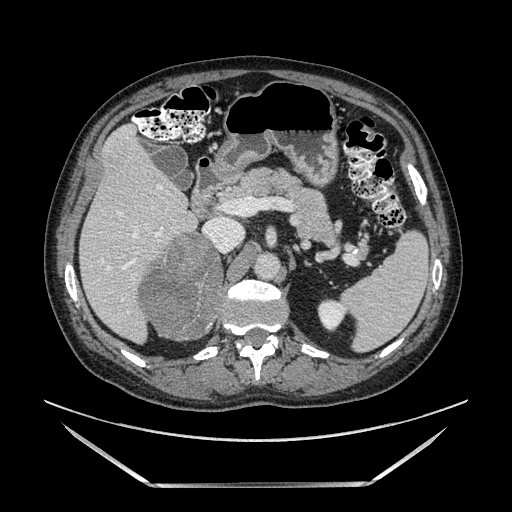
Contrast-enhanced abdominal CT, one axial slice. Position 83 of 185 along the scan axis. Soft-tissue window (W 400 / L 40 HU). 1.25 mm slice thickness. 512 × 512 image matrix, field of view 440 × 440 mm. Male patient. From the clinical record (not read from this slice): diagnosis: adrenocortical carcinoma; tumour side: right adrenal; tumour size at pathology: 10.3 cm; Ki-67 index: 20 %; stage (as recorded): 3.
Outlined on this slice (semi-automatically segmented with operator editing):
- mass: bounding box <143,230,220,344> (left, top, right, bottom; pixels)